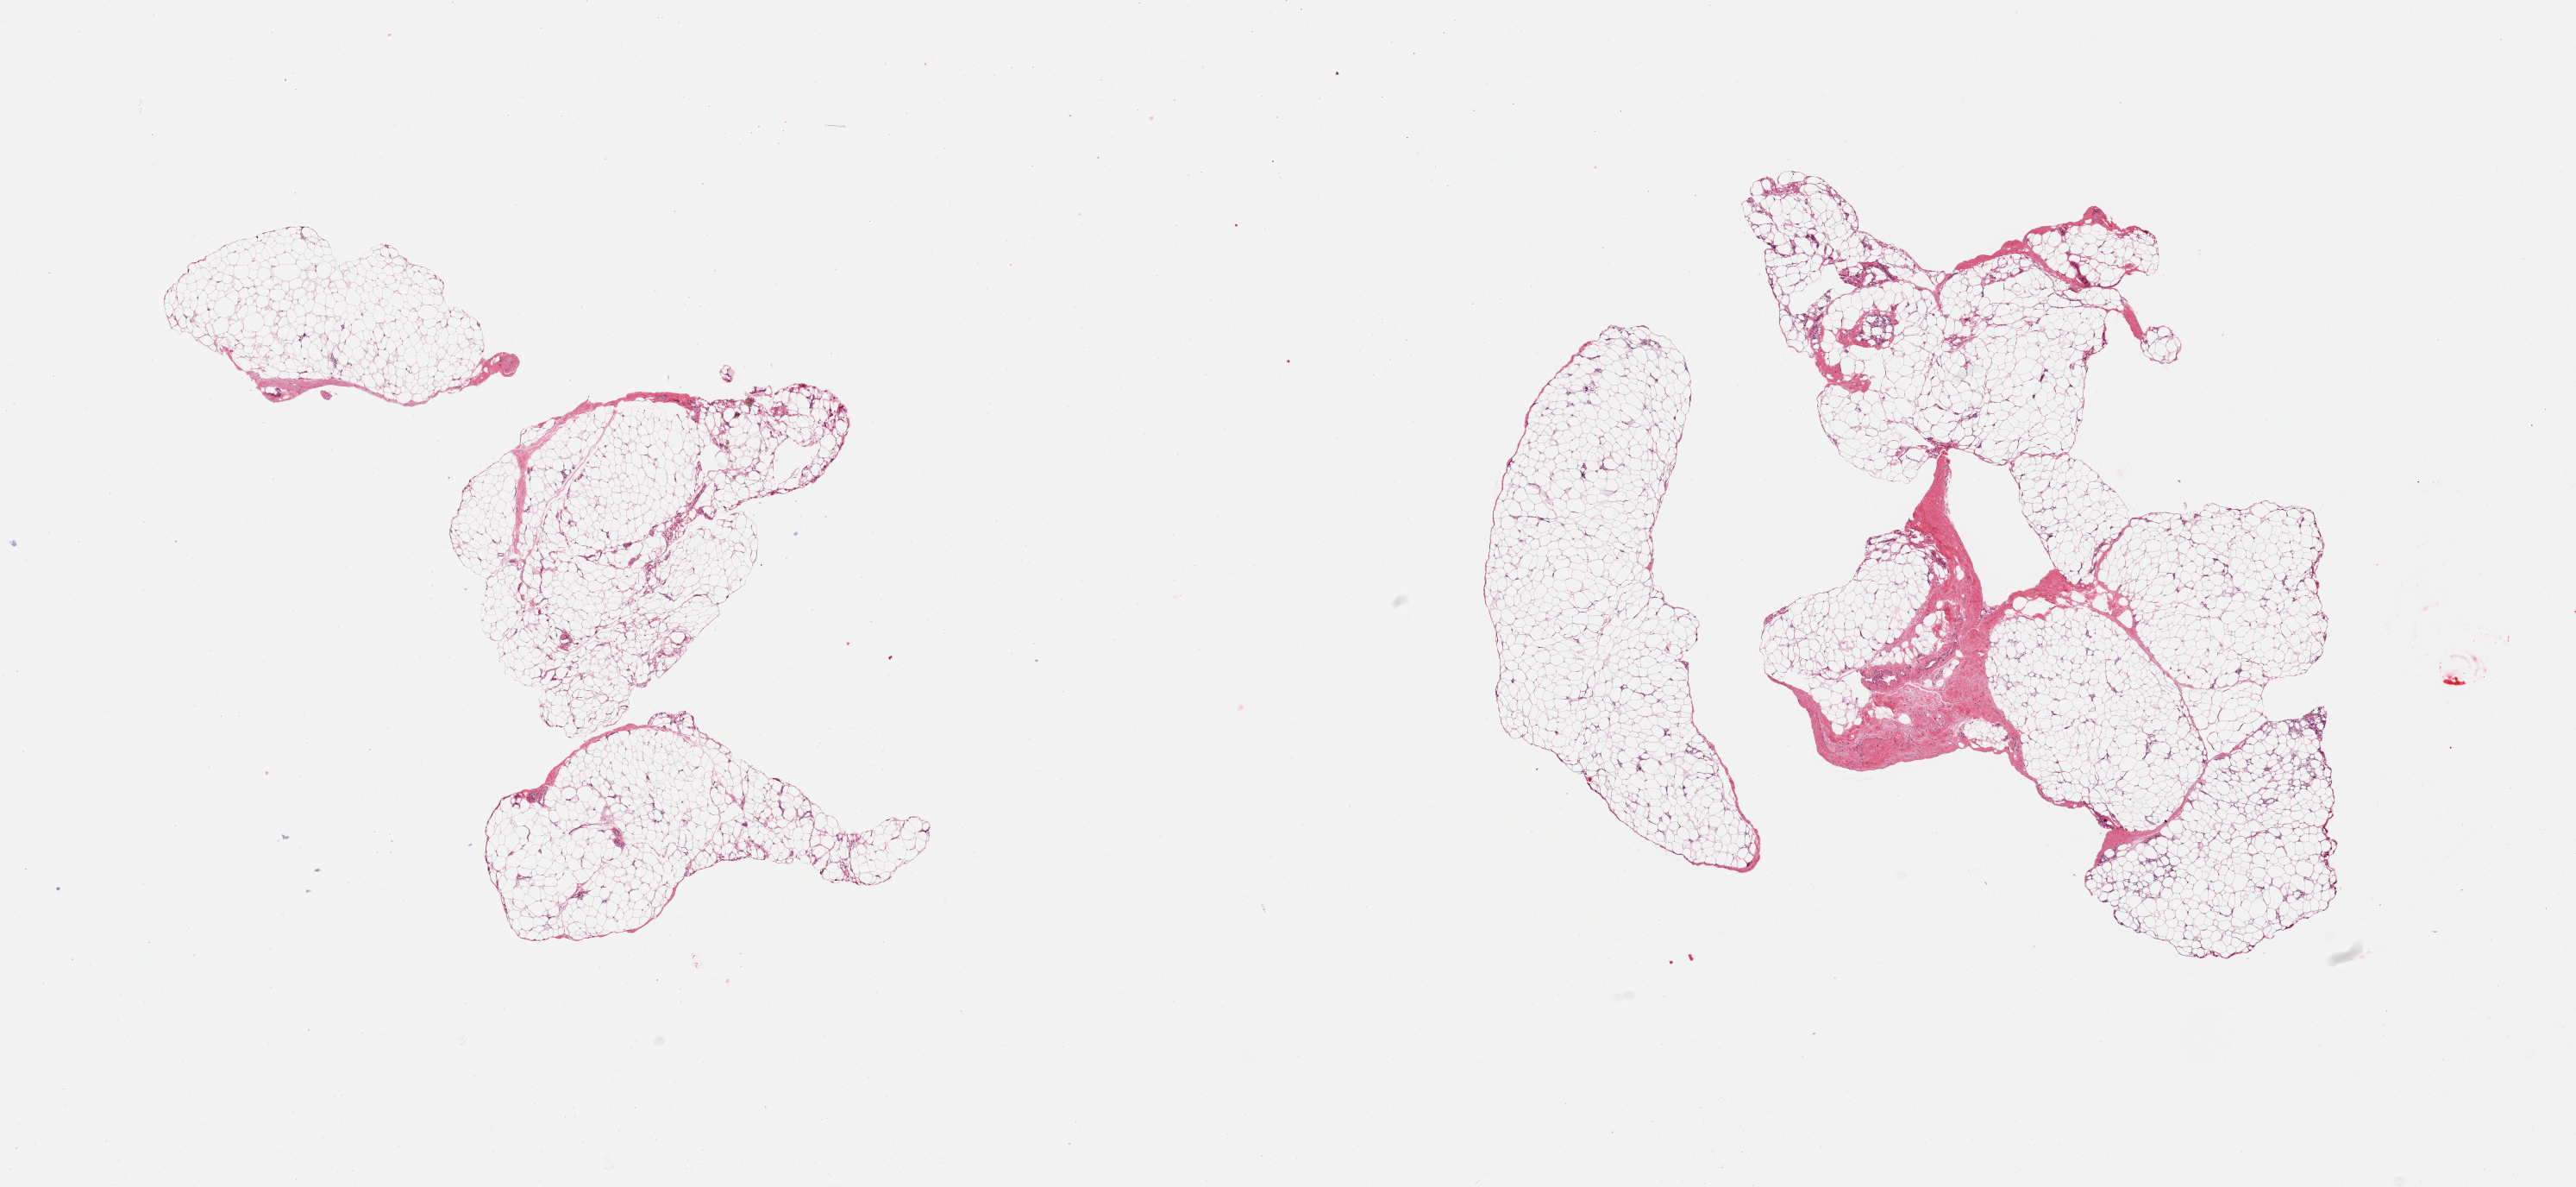
Digitized H&E-stained section — a low-resolution overview of the entire scanned area, about 23.6 x 10.9 mm; PAXgene-fixed, paraffin-embedded tissue; sampled site (target tissue): adipose tissue; donor tissue sample. Donor: male.
- reviewer comment on this tissue sample: 2 pieces